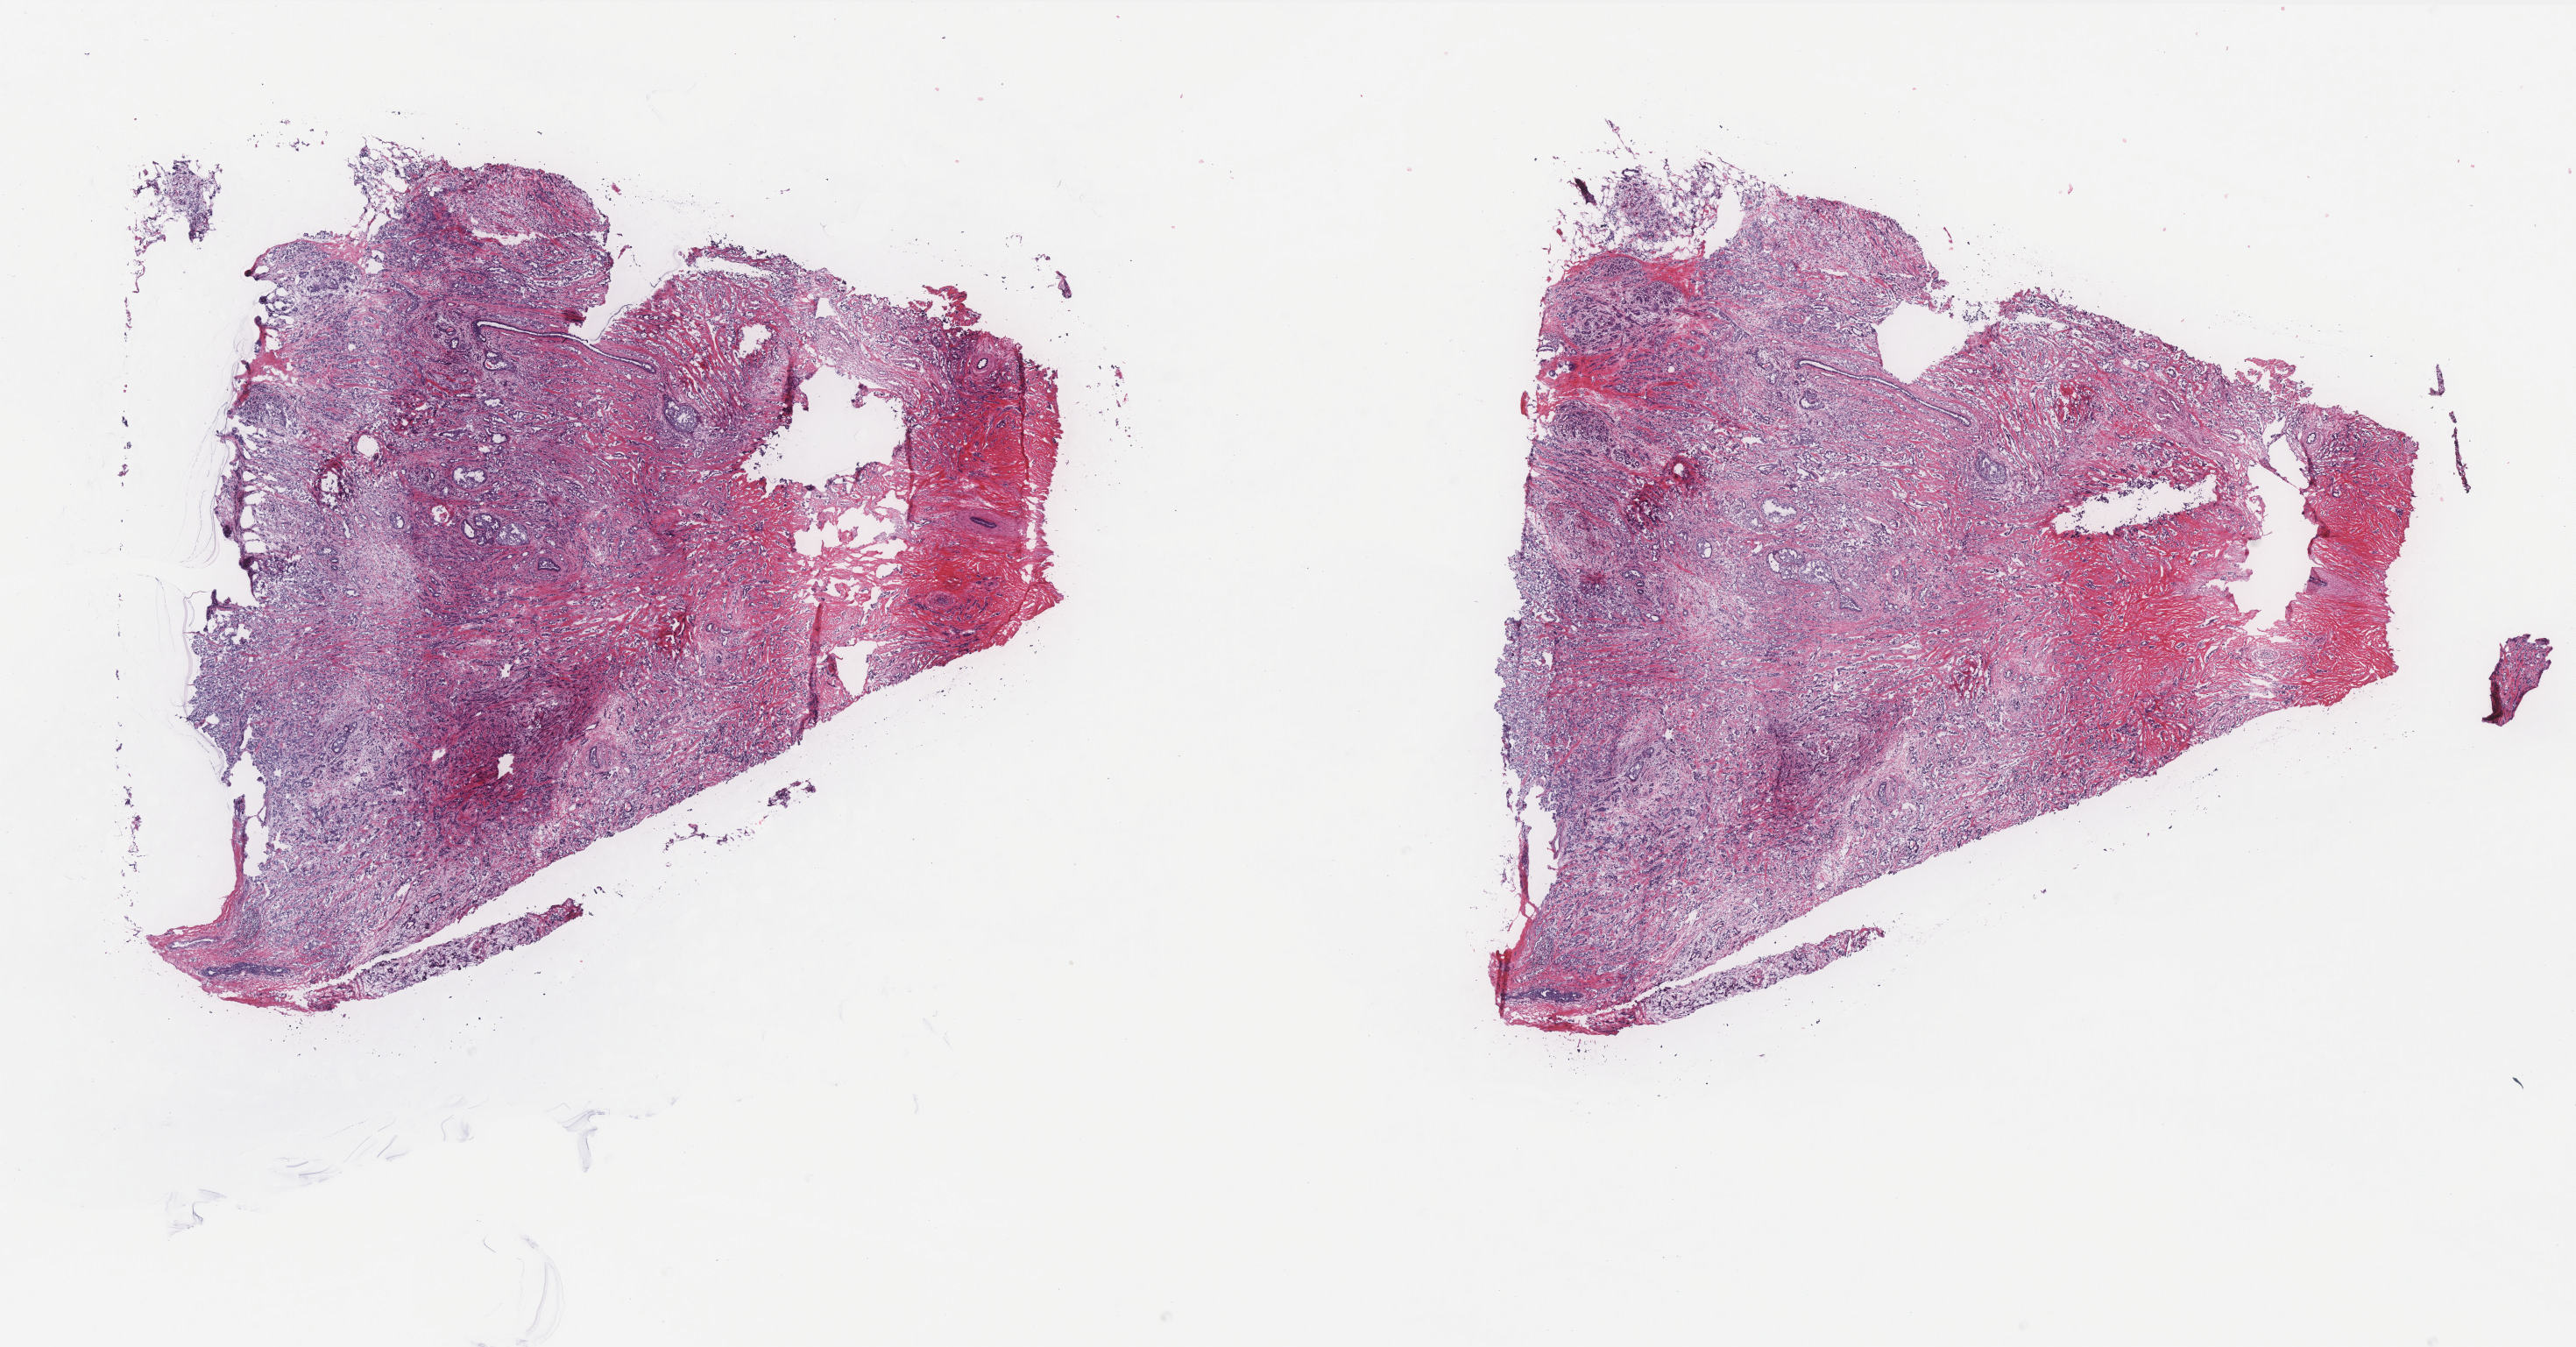
H&E-stained whole-slide image, whole scanned area (about 23.6 x 12.3 mm, acquisition: 40x scan) shown as a low-resolution overview; frozen section from the top of the tissue portion; sample: primary tumour, breast. Patient: female, age at initial diagnosis 42 years. Pathologist review of this section (percent, as recorded): tumour cells 60%, tumour nuclei 80%, normal cells 7%, stromal cells 33%, necrosis 0%. Infiltration values recorded for this section: lymphocyte infiltration 2%, monocyte infiltration 0%, neutrophil infiltration 0%.
Diagnosis: Infiltrating duct carcinoma, NOS. Laterality: left. AJCC pathologic stage: IIB (6th edition). TNM: T2 N1a M0.